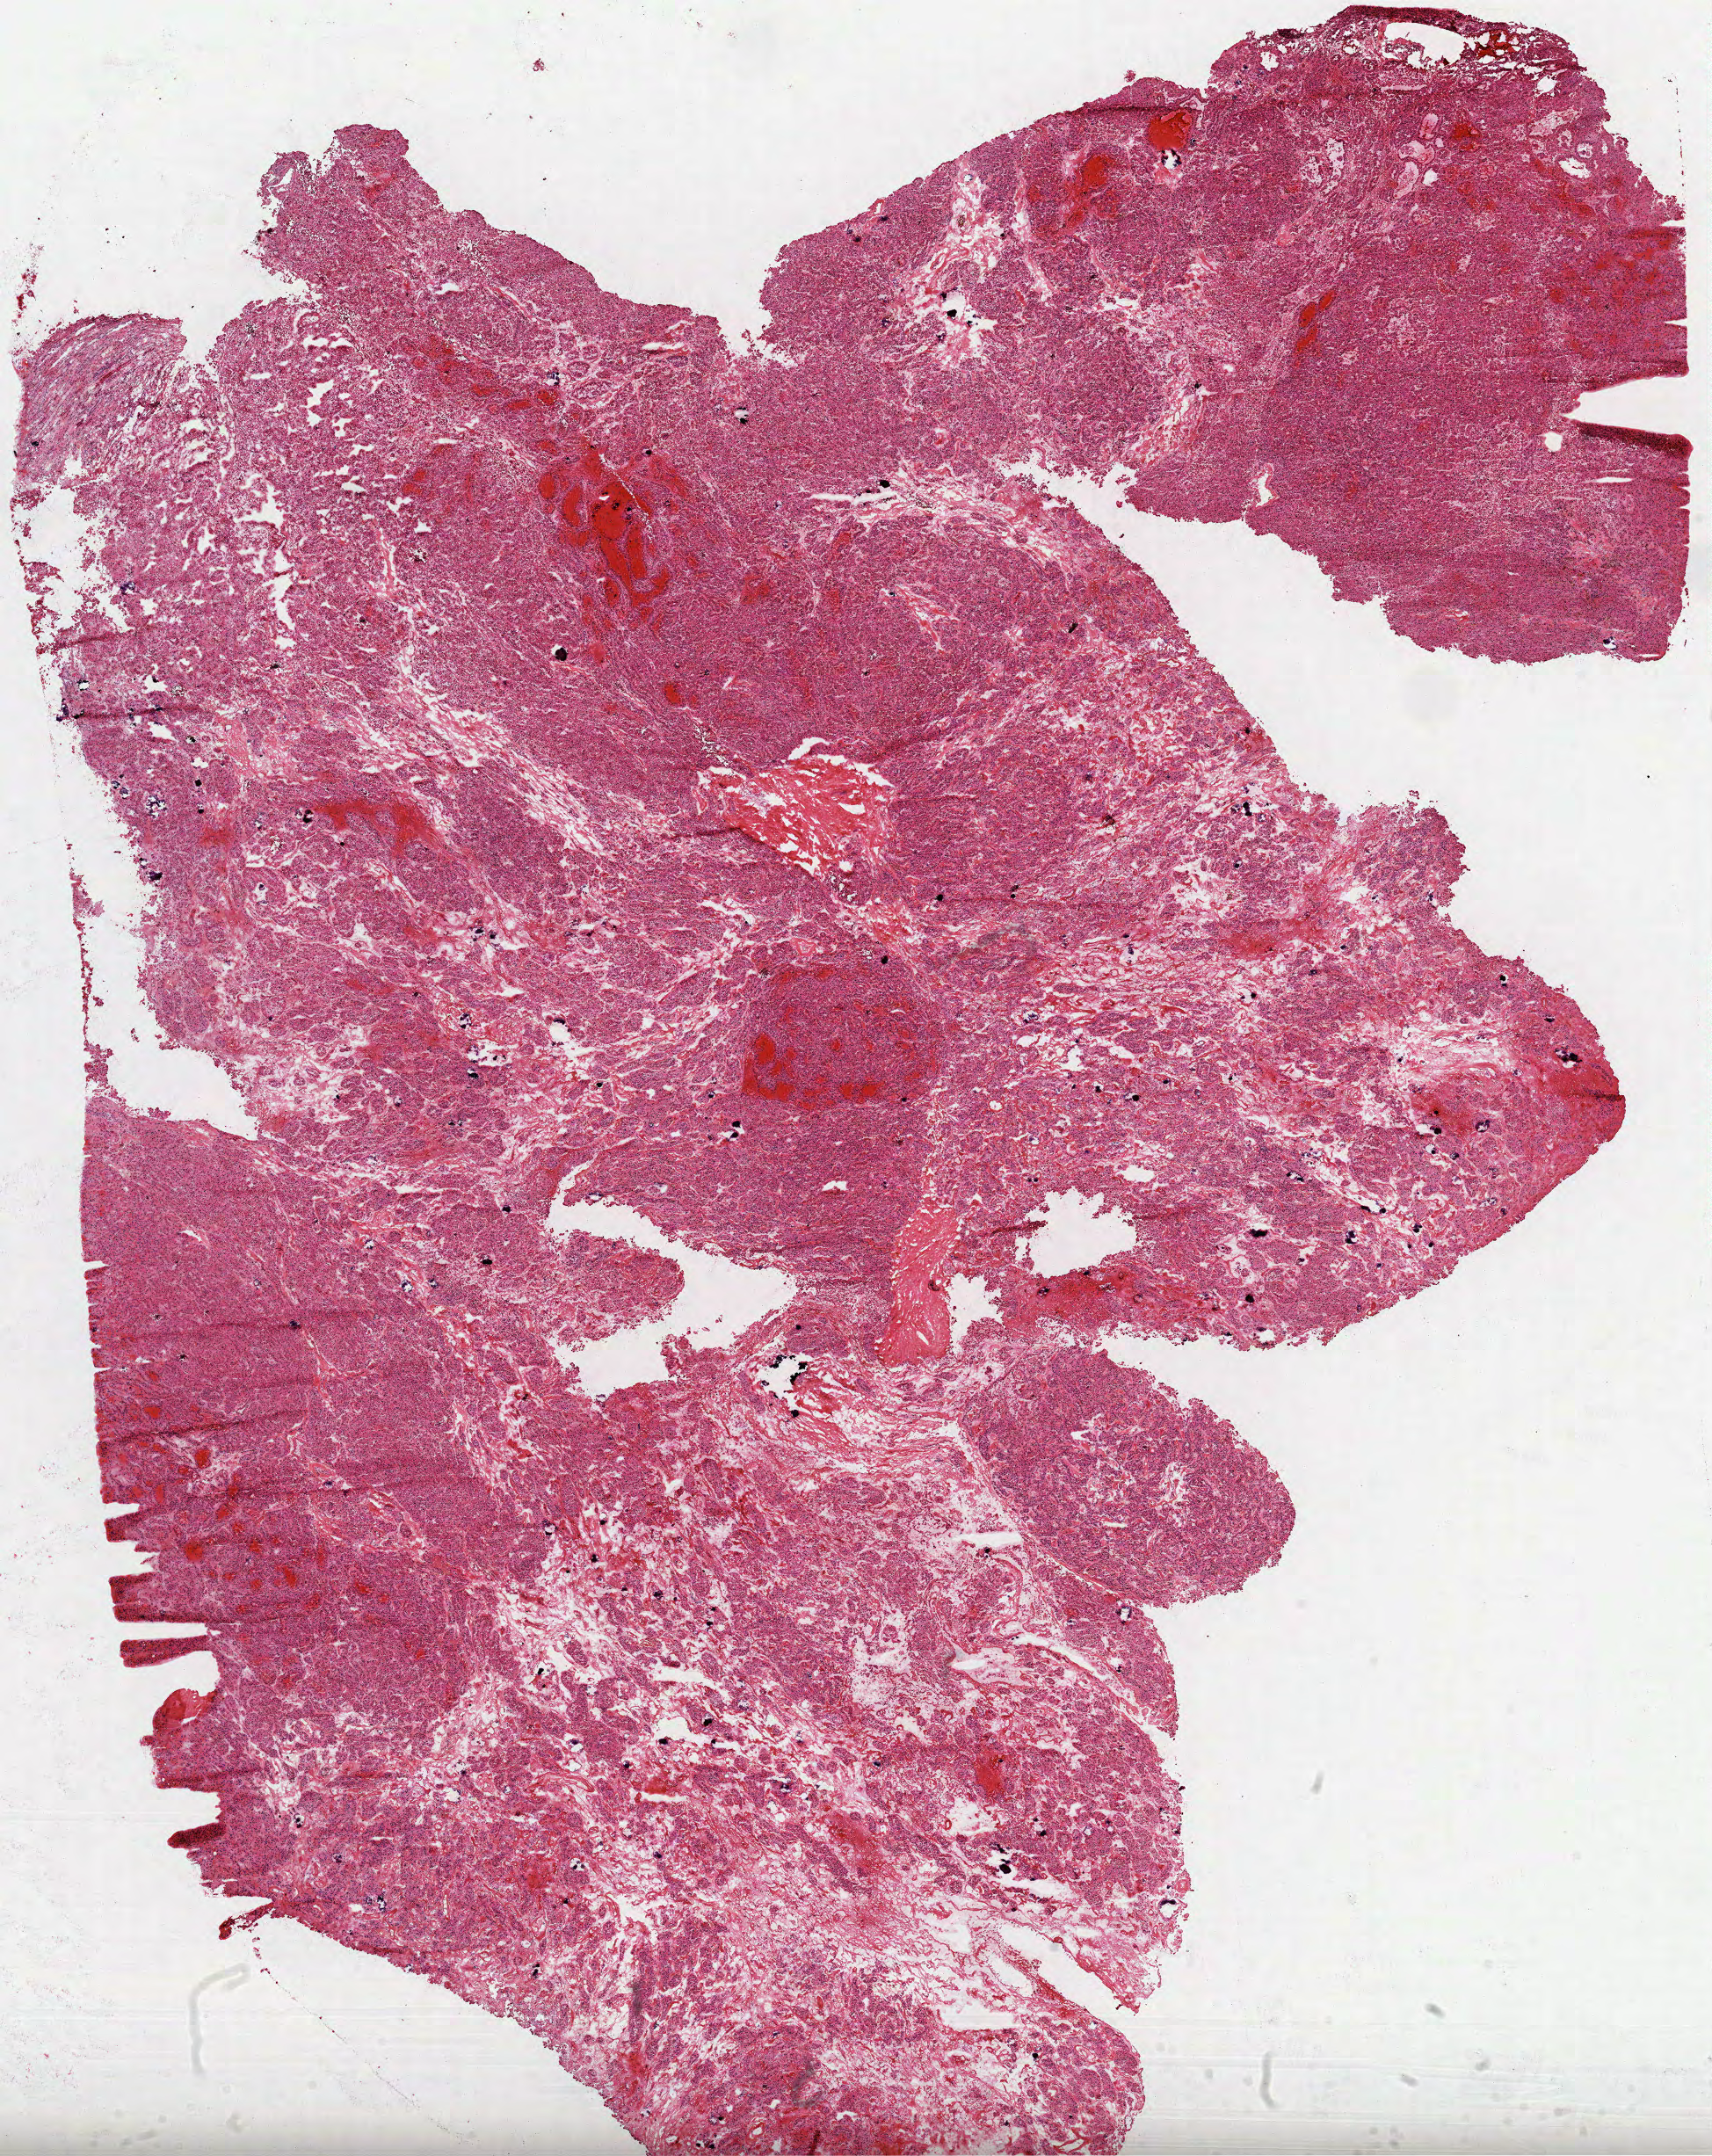
Digitized H&E-stained tissue section (whole slide) — a low-resolution overview of the entire scanned area, about 15.7 x 19.8 mm, frozen section, kidney, primary tumour sample. Male patient; age at initial diagnosis 73 years. Composition of this section per pathologist review: tumour cells 100%, tumour nuclei 80%, normal cells 0%, stromal cells 0%, necrosis 0%. Inflammatory infiltration, as recorded: lymphocyte infiltration 3%, monocyte infiltration 5%, neutrophil infiltration 0%.
Diagnosis: Papillary adenocarcinoma, NOS. AJCC pathologic stage: I (6th edition). TNM: T1a NX M0.